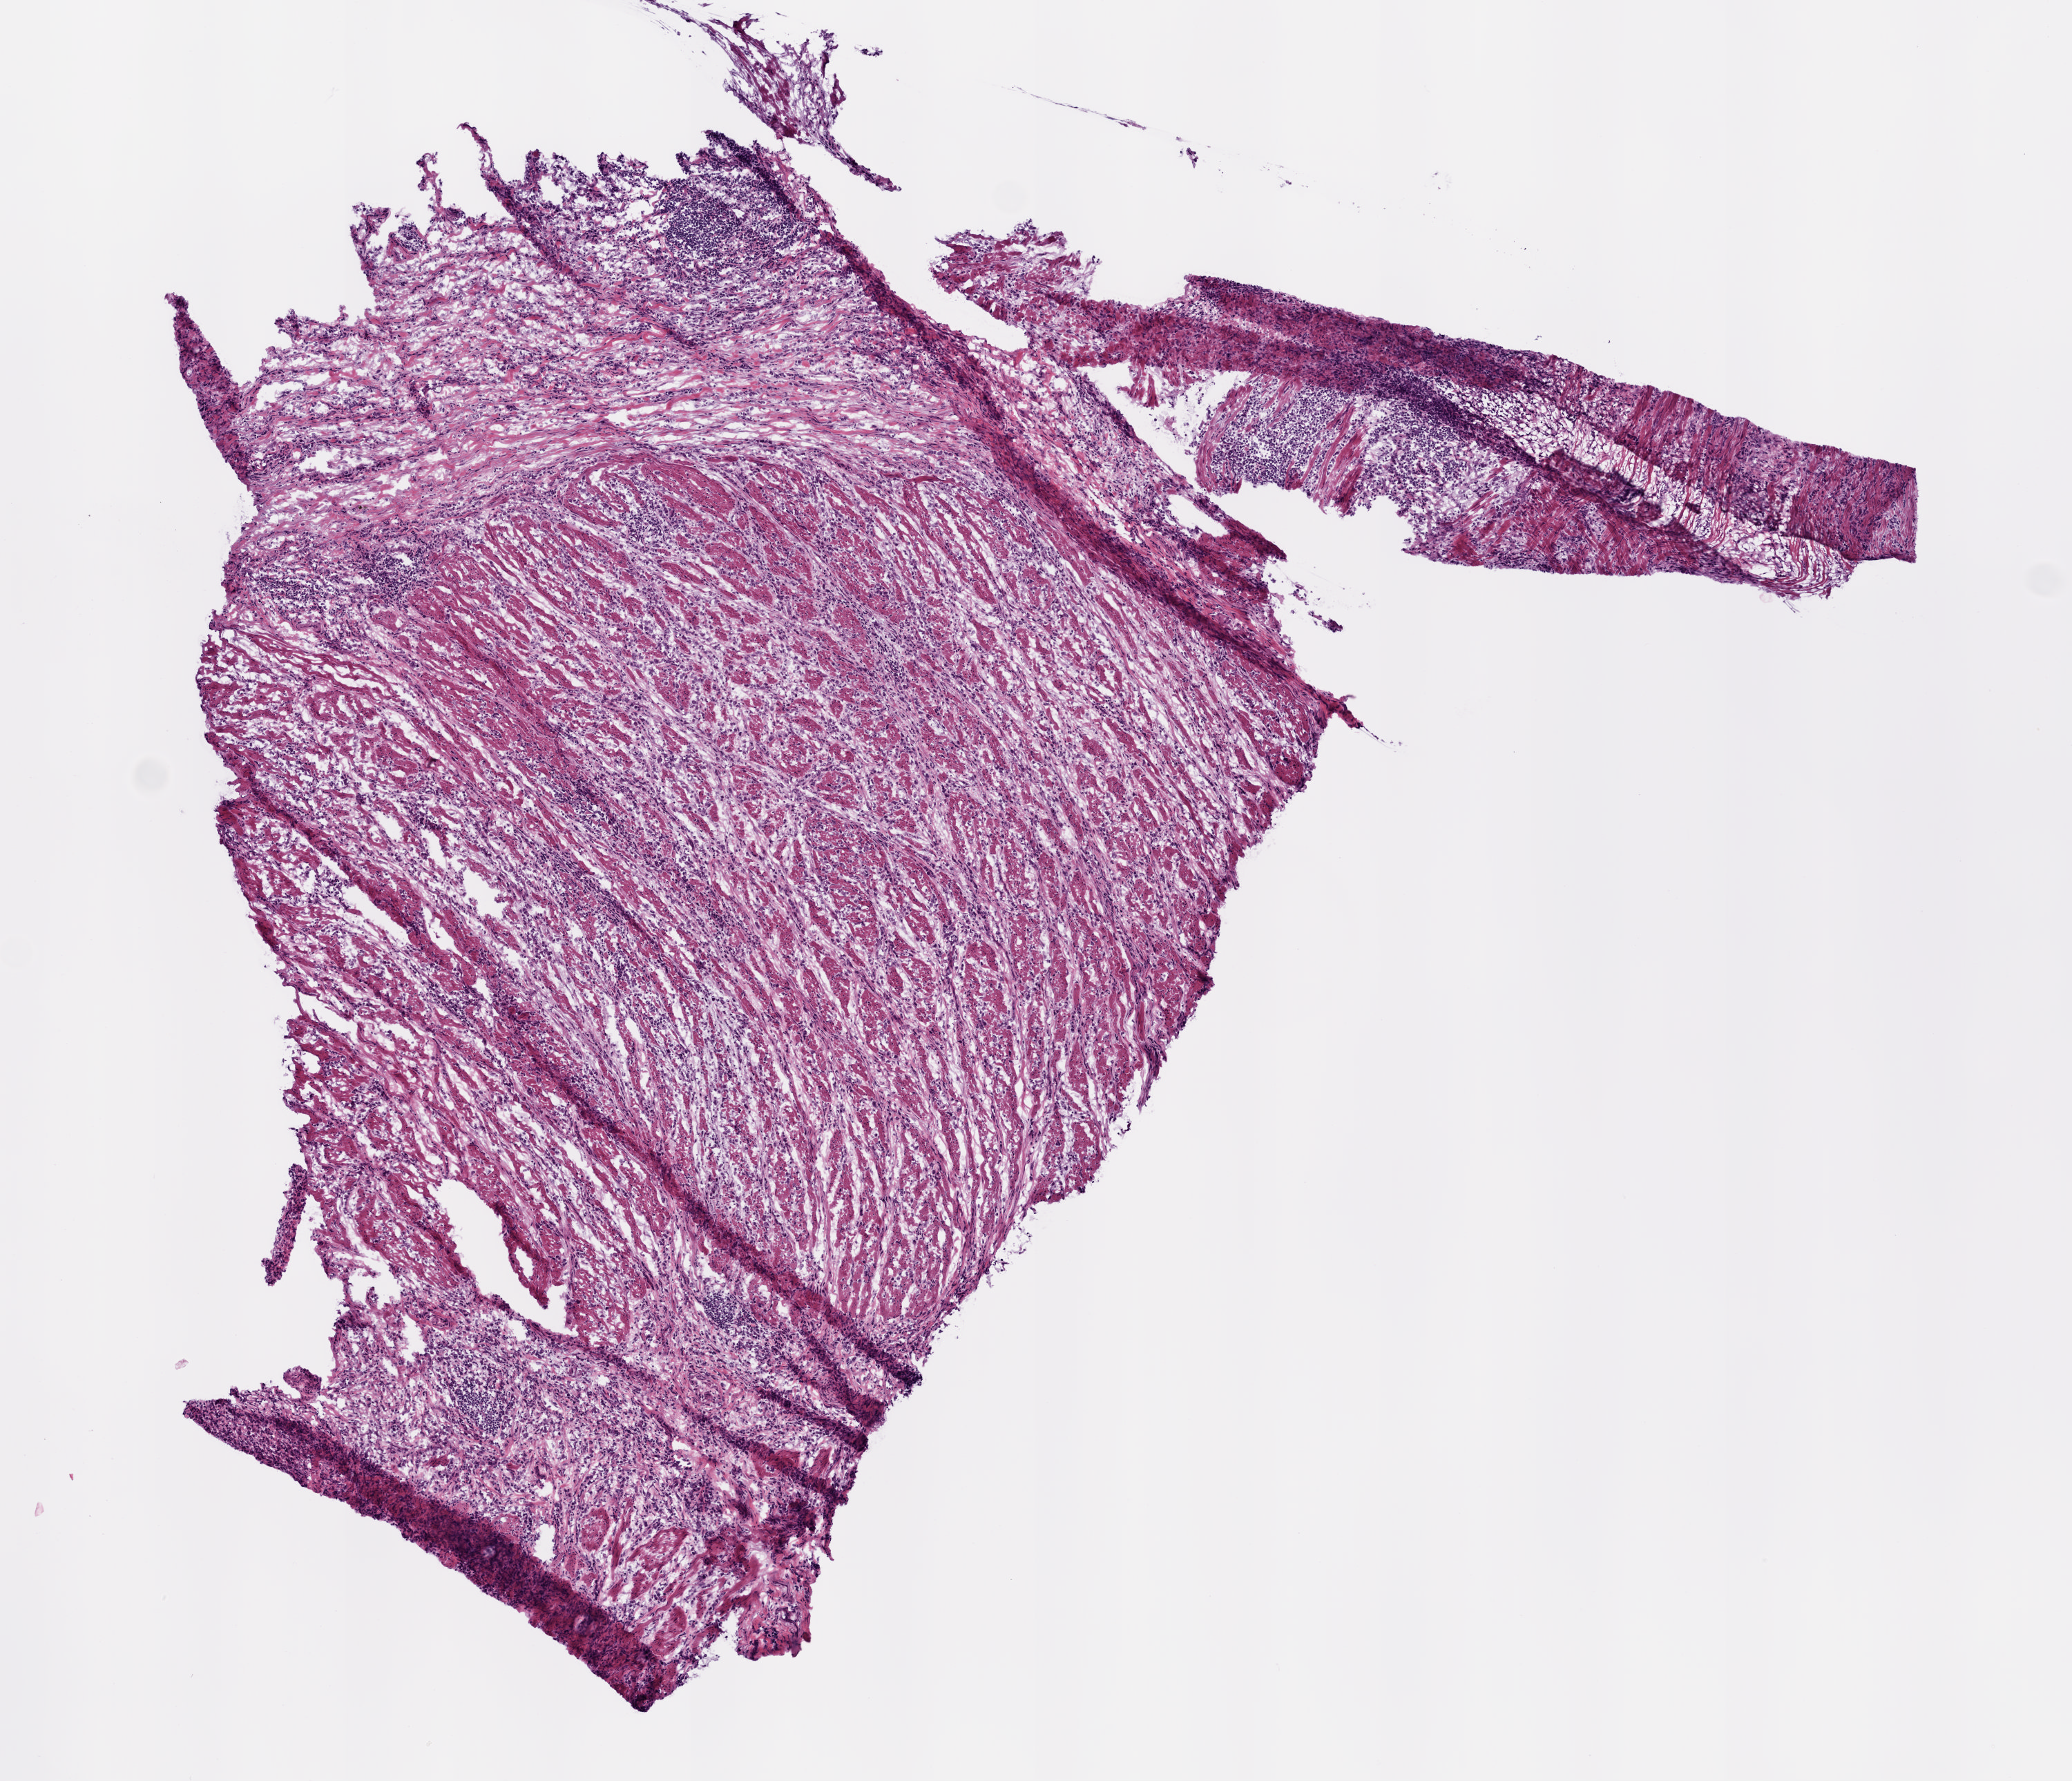
Whole-slide histology image, H&E — a low-resolution overview of the entire scanned area, about 6.0 x 5.2 mm; frozen section from the bottom of the tissue portion; sample: primary tumour, stomach. Male patient; age at initial diagnosis 58 years. Pathologist review of this section (percent, as recorded): tumour cells 60%, tumour nuclei 75%.
Pathologic diagnosis: Adenocarcinoma, intestinal type.